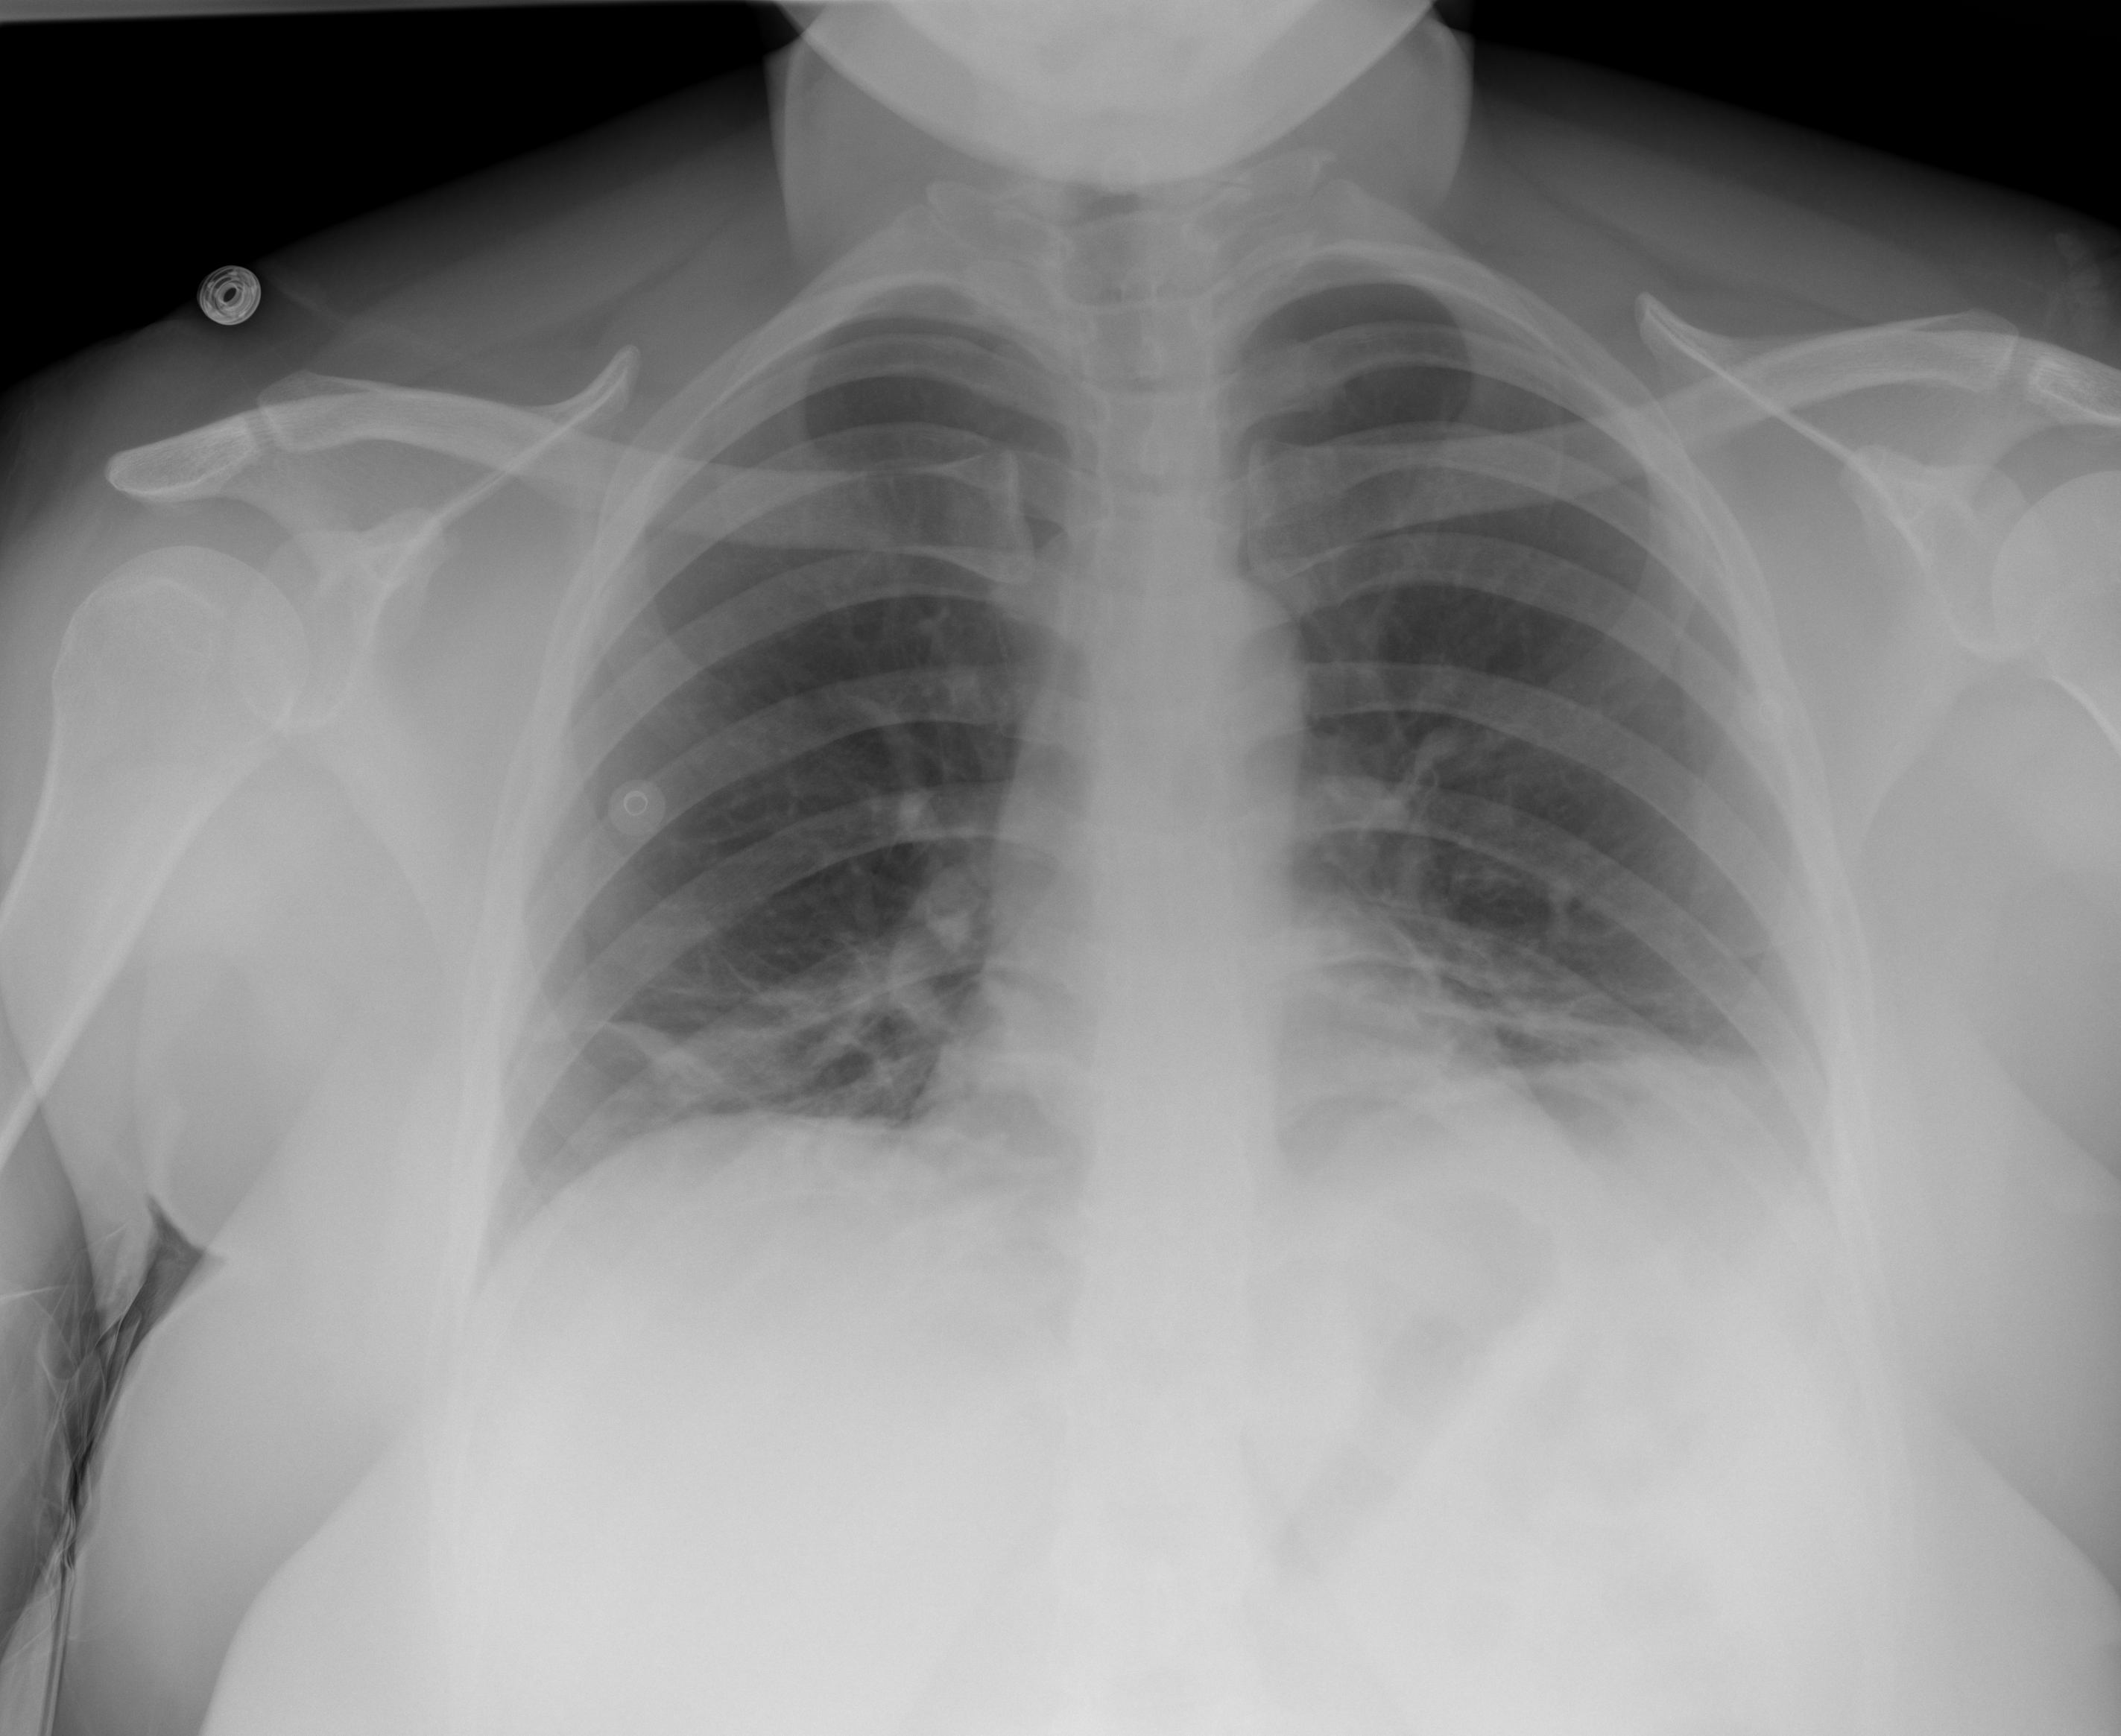
Chest X-ray (portable), AP projection. Female patient, age 34 years; imaged 4 days after the COVID-19 diagnosis.
Radiologist's key findings for this exam: Streaky opacities at both lung bases.